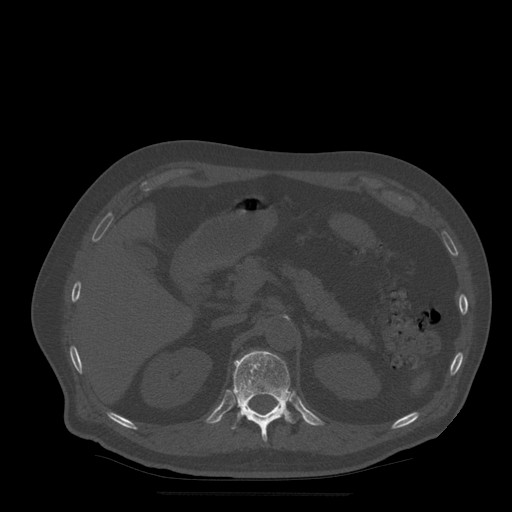
CT including the spine, one axial slice. Slice 218 of 522 in the series (ordered by position). Bone window (W 1800 / L 400 HU). 512 × 512 image matrix, field of view 420 × 420 mm. Patient age 72 years. Case-level facts recorded for this patient, not image findings: primary cancer: prostate.
Annotated regions visible in this slice (semi-automatic segmentation, software-assisted and operator-edited):
- T12 vertebra: bounding box <232,351,295,442> (left, top, right, bottom; pixels)